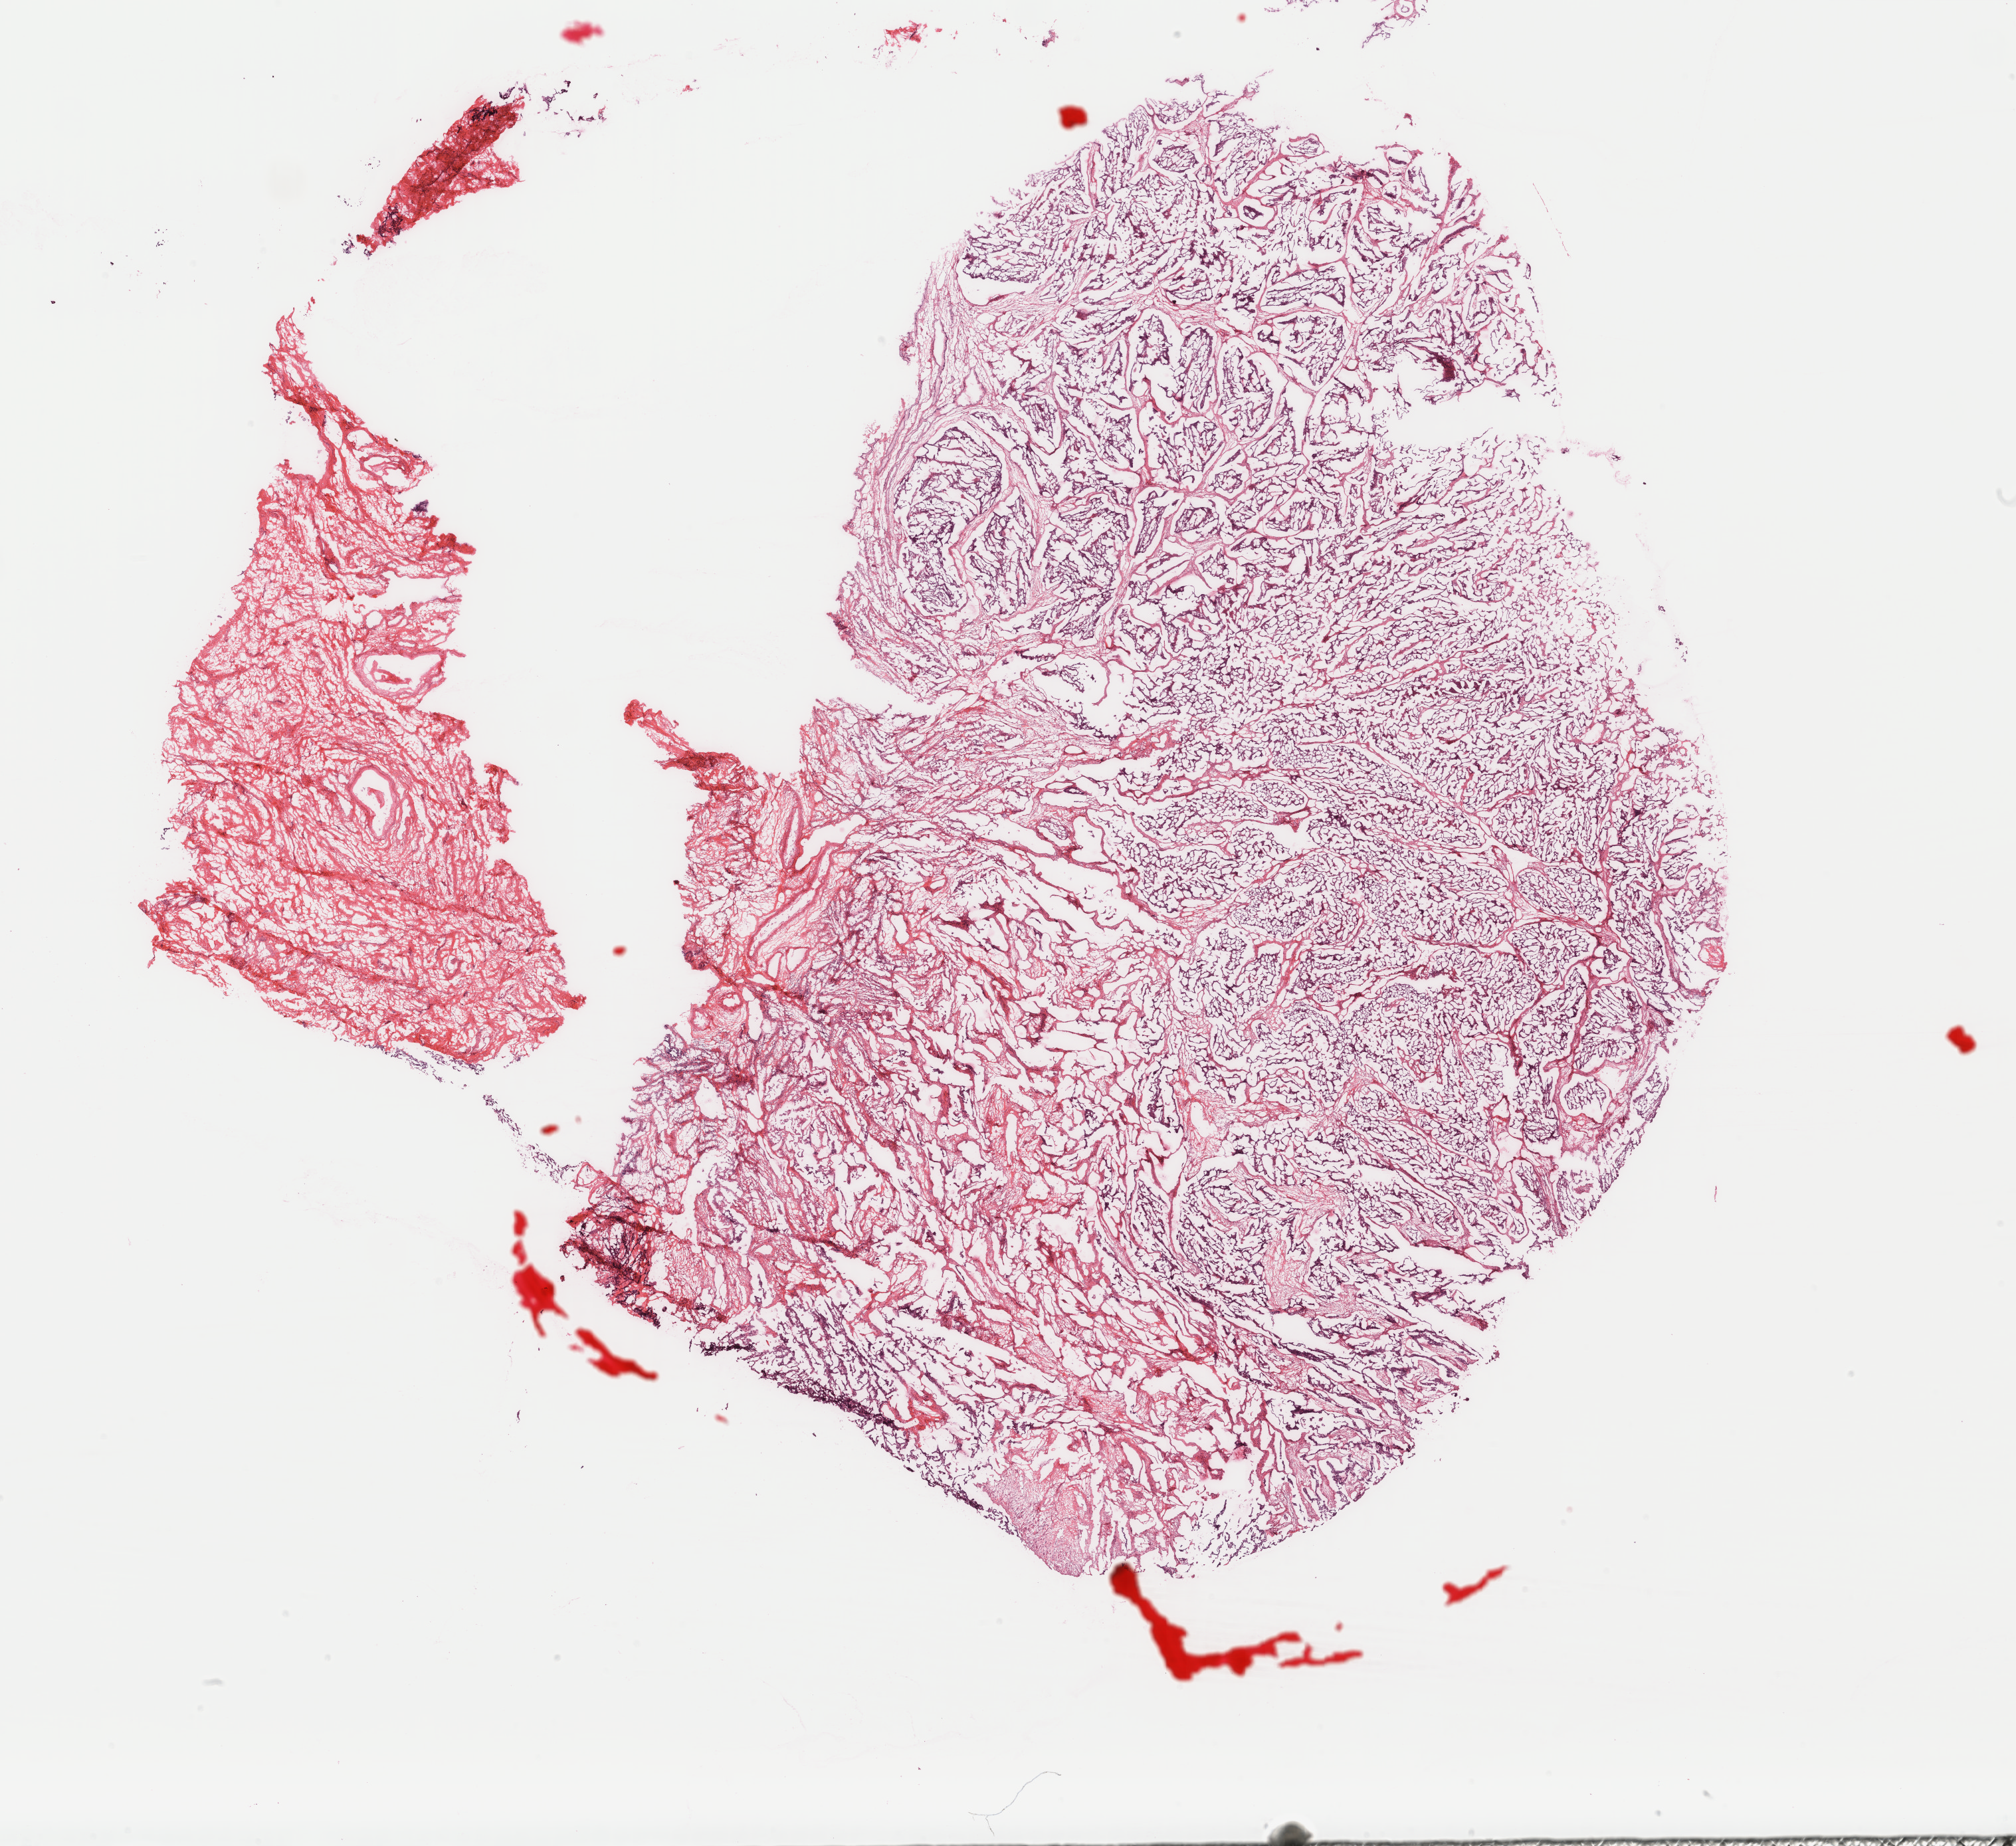
Whole-slide histology image, H&E, whole scanned area (about 24.1 x 22.0 mm, from a 40x scan) shown as a low-resolution overview; formalin-fixed paraffin-embedded (FFPE) diagnostic section; primary tumour sample from the cervix. Patient: female, age at initial diagnosis 49 years. Histologic grade: G2 (moderately differentiated).
Pathologic diagnosis: Adenocarcinoma, endocervical type (cervix uteri). FIGO stage: IB2.